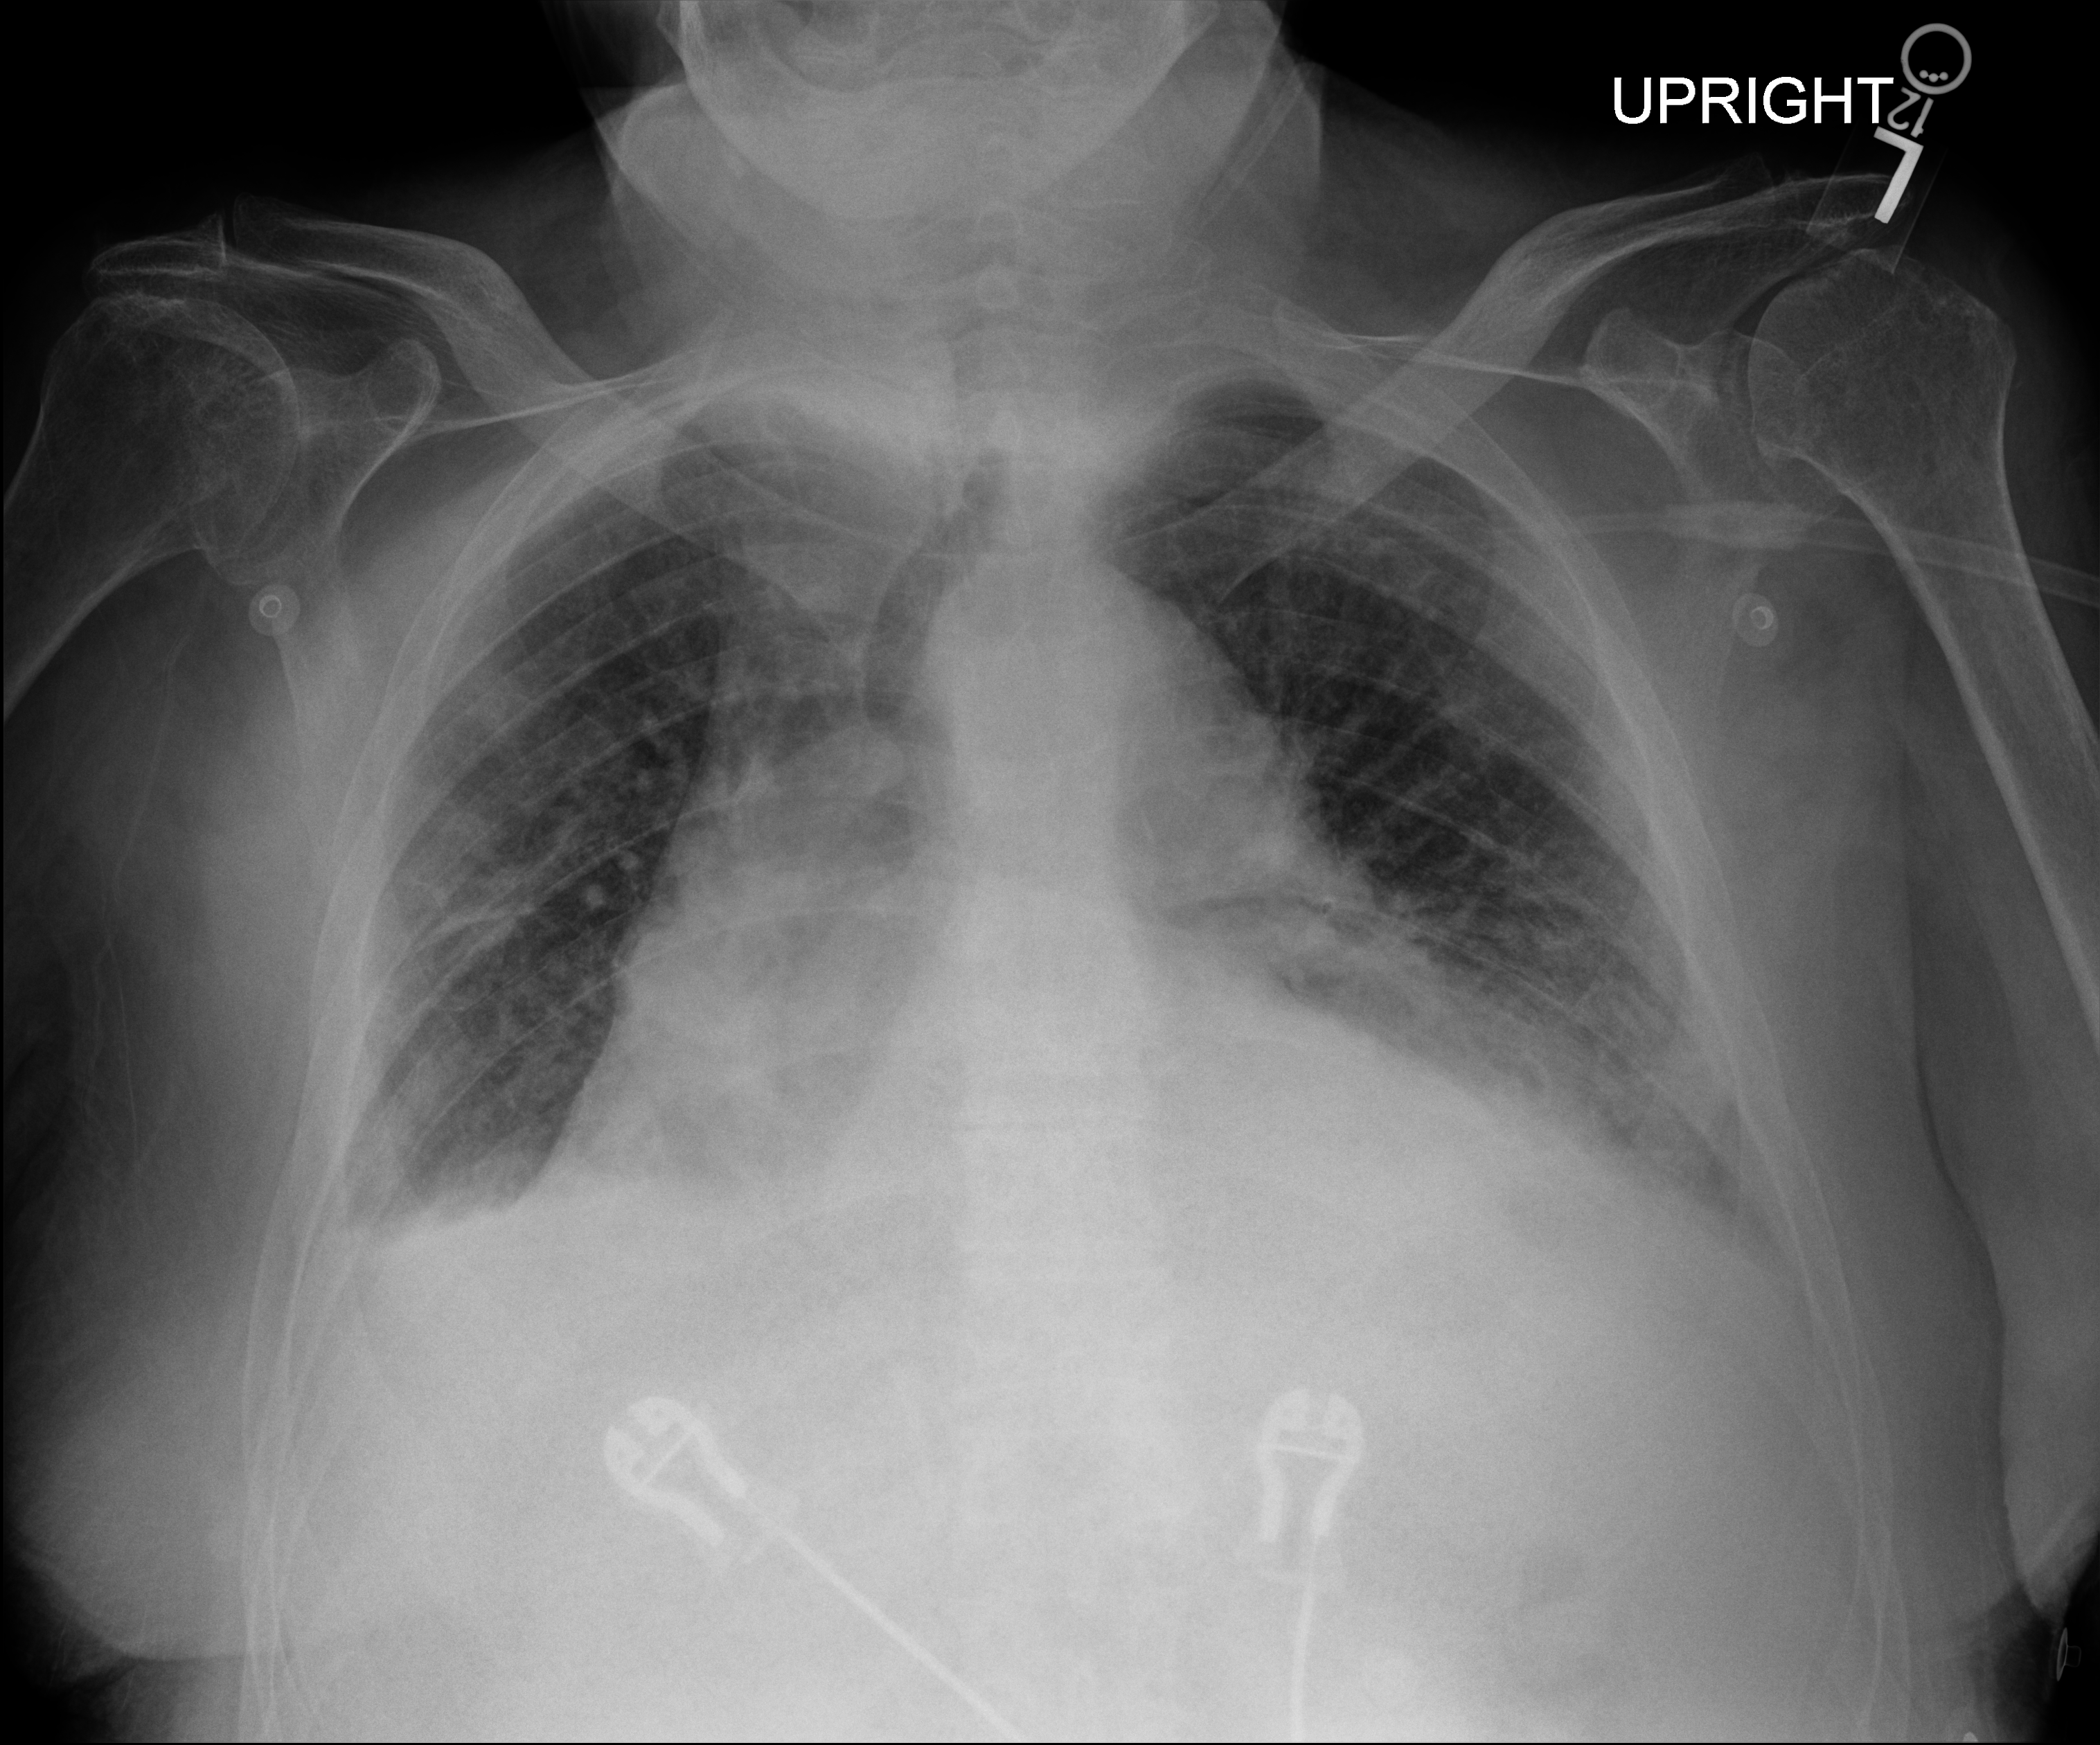
Chest radiograph; anteroposterior (AP) projection. Male patient hospitalised with COVID-19, age 75–90 years.
Admission-level facts for this patient (not findings on this image; timing relative to this image not recorded):
- chronic kidney disease (admission record): yes